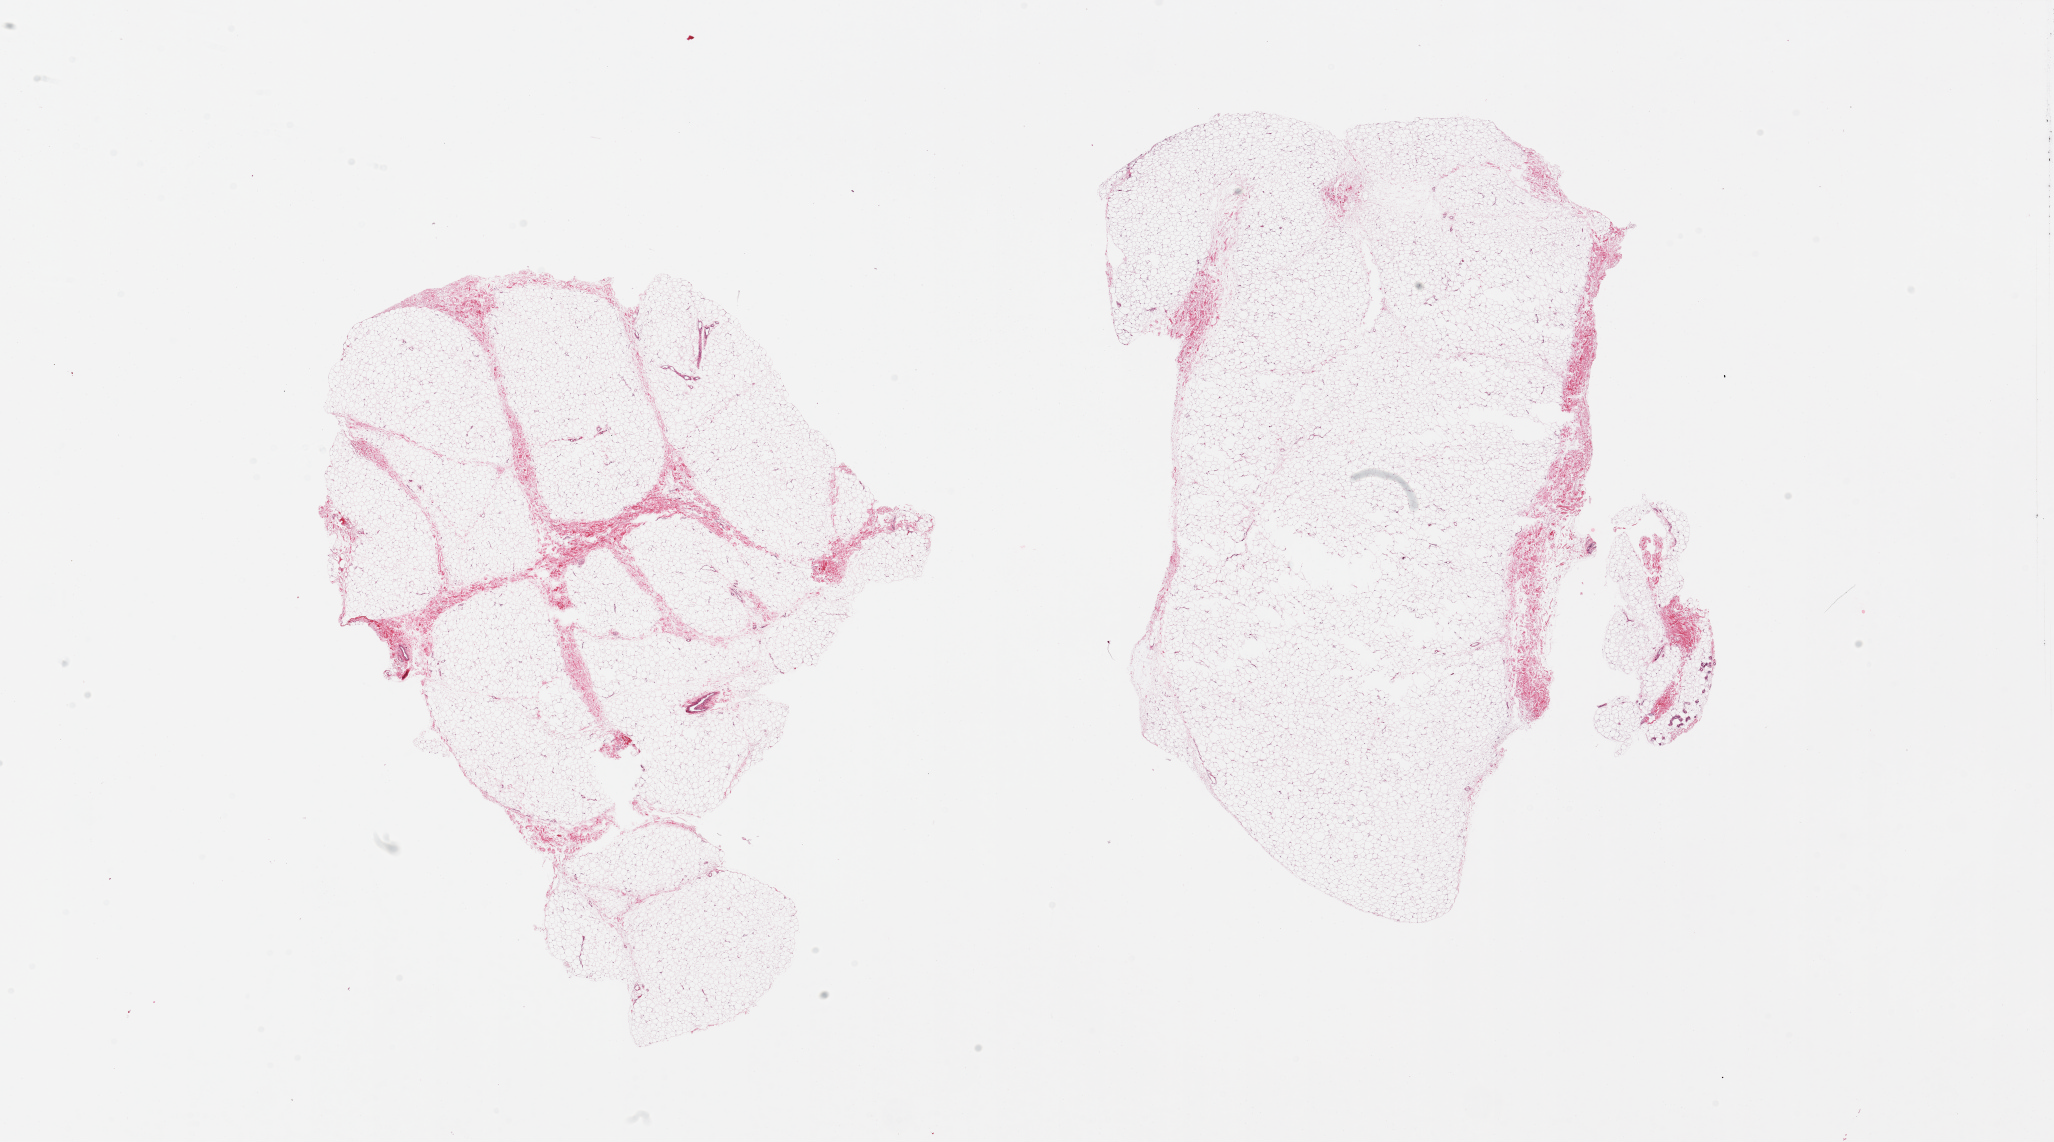
Digitized haematoxylin and eosin-stained section — shown as a low-resolution overview of the whole scanned area (about 32.5 x 18.1 mm), PAXgene-fixed, paraffin-embedded tissue, sampled site (target tissue): adipose tissue, tissue donor sample. Female donor.
• review note (as recorded): 2 pieces. 12x9.5 & 12.5x11mm